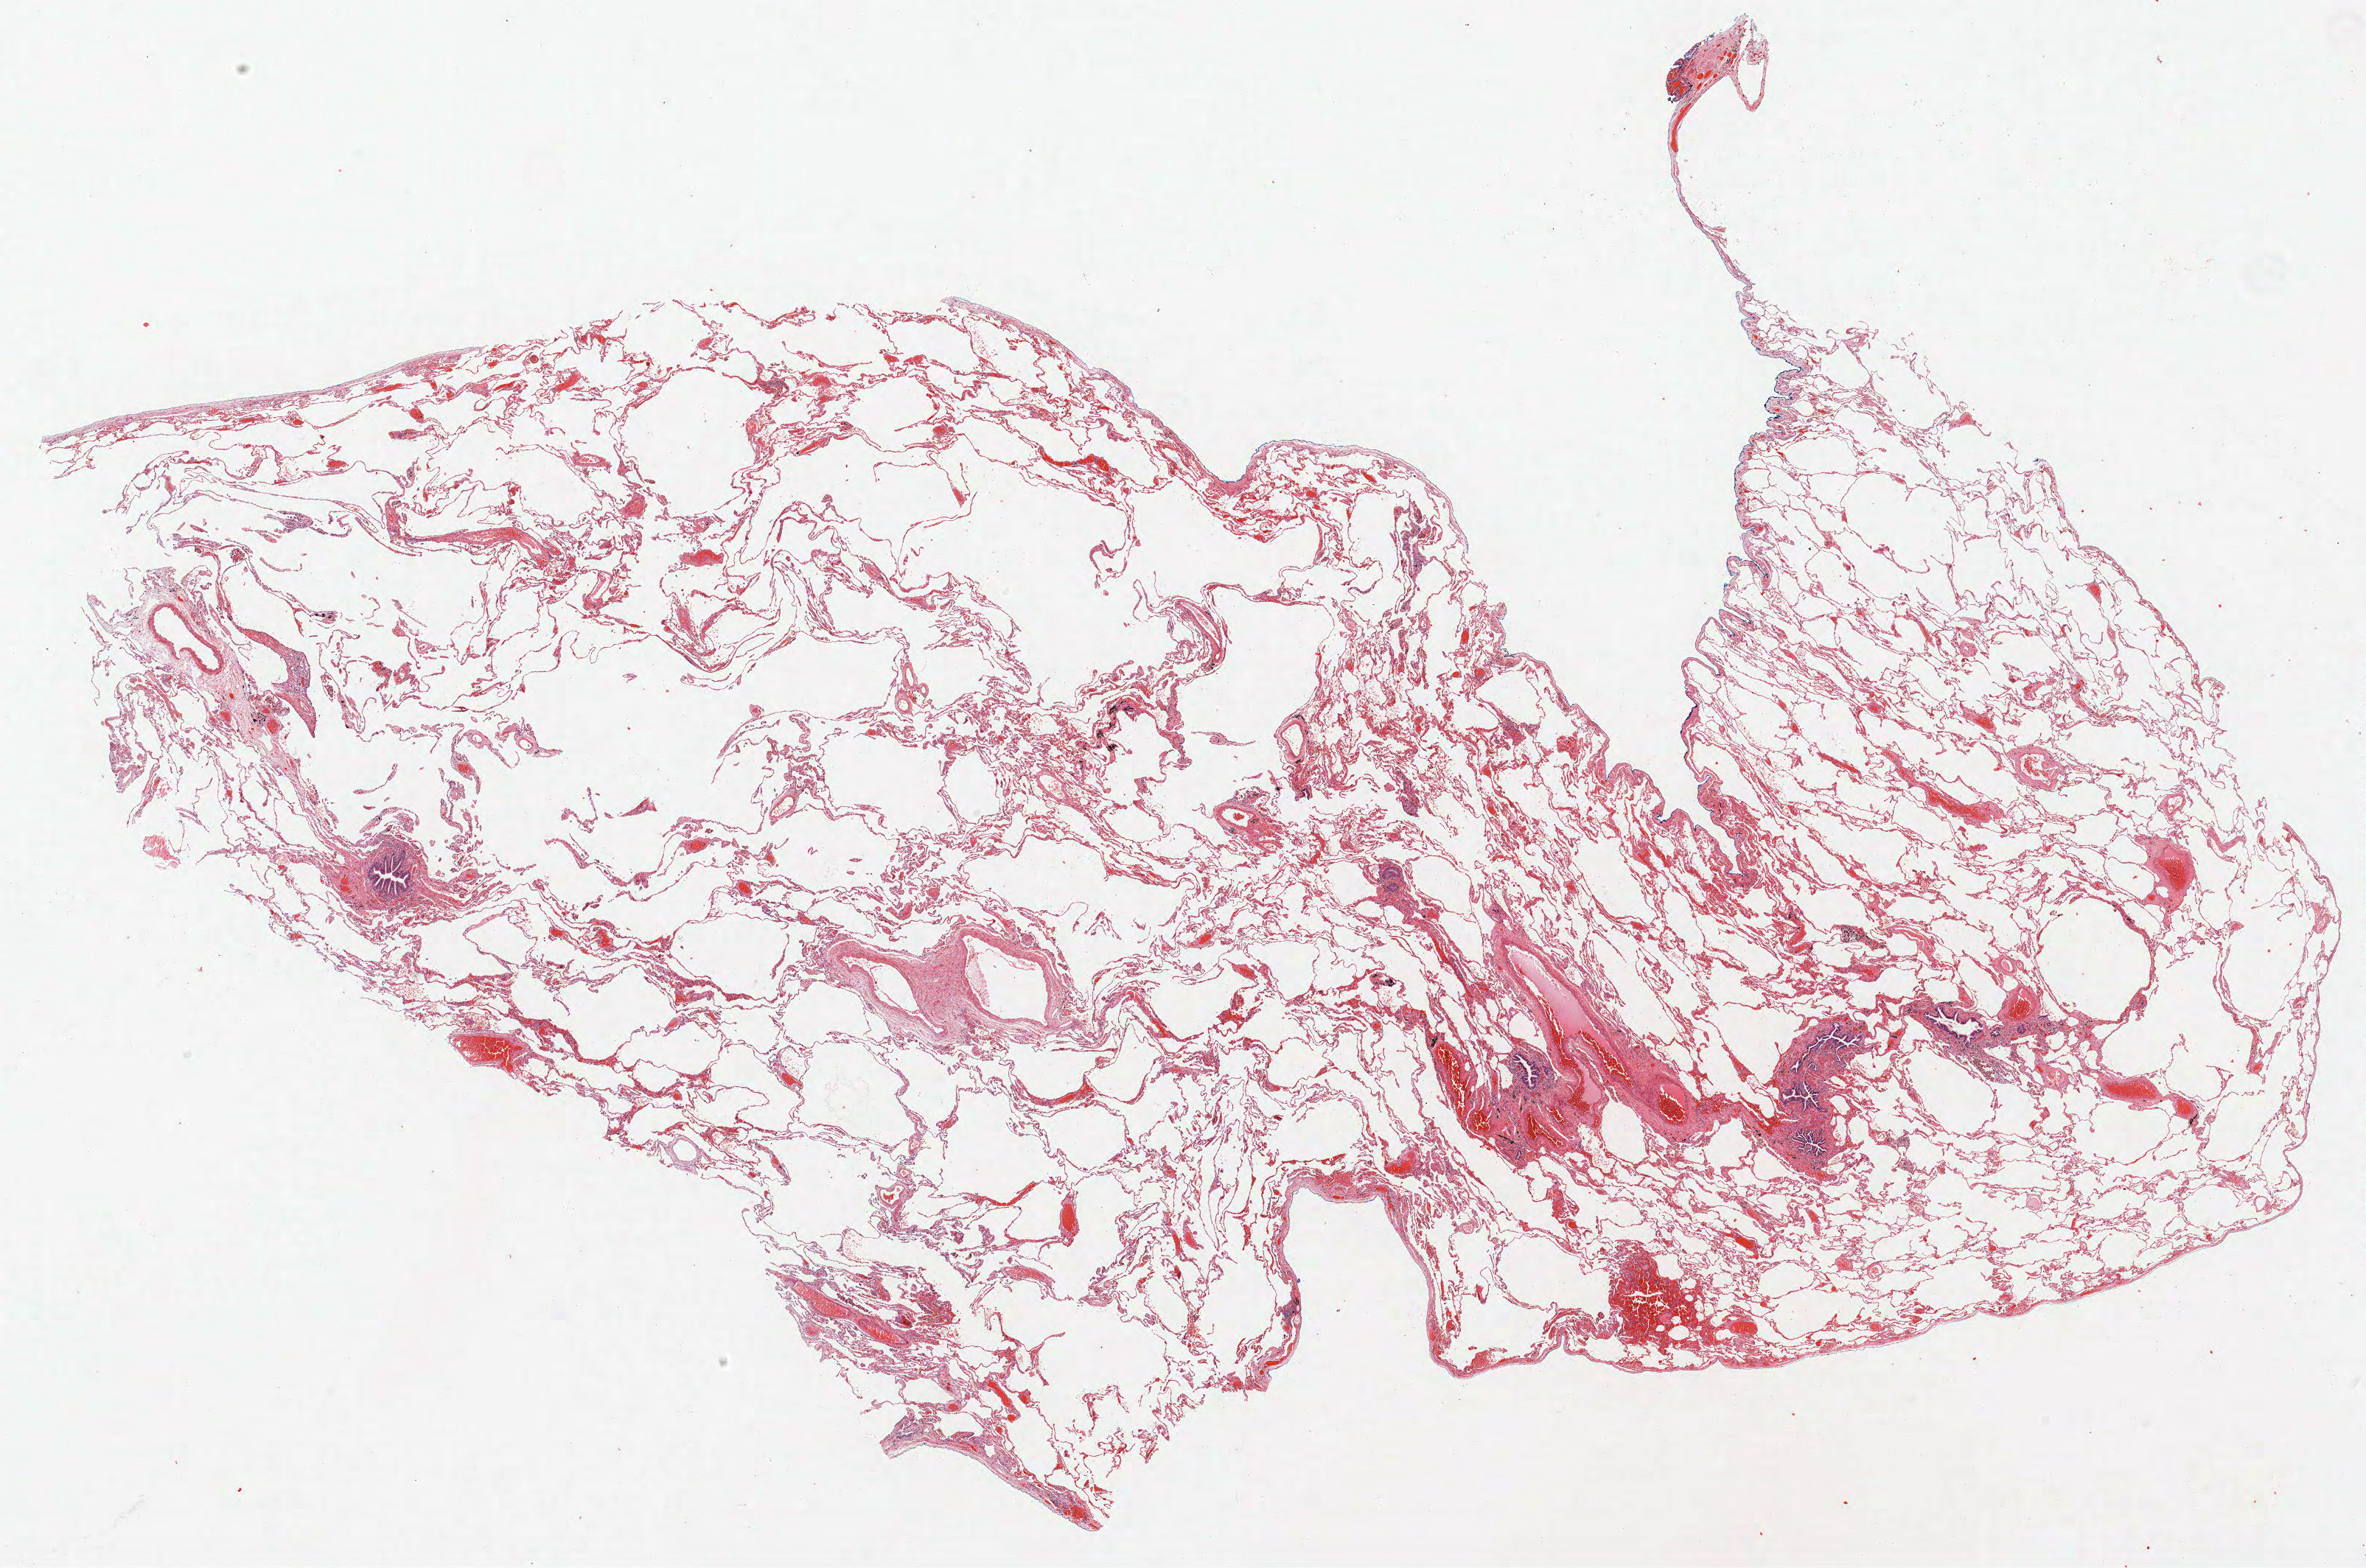
Whole-slide histology image, Hematoxylin and eosin (H&E) stained — shown as a low-resolution overview of the whole scanned area (about 25.7 x 17.0 mm, acquisition: 40x scan), FFPE section, lung tissue. Male patient, aged 58 at enrolment. Grade: moderately differentiated (G2).
- stage (AJCC 6th edition): IA
- participant's lung-cancer diagnosis: Squamous cell carcinoma, large cell, nonkeratinizing, NOS (ICD-O-3 8072/3)
- primary tumour location (clinical record): right lower lobe
- ICD-O-3 topography: lower lobe of lung (C34.3)
- tumour size (pathology): 11 mm